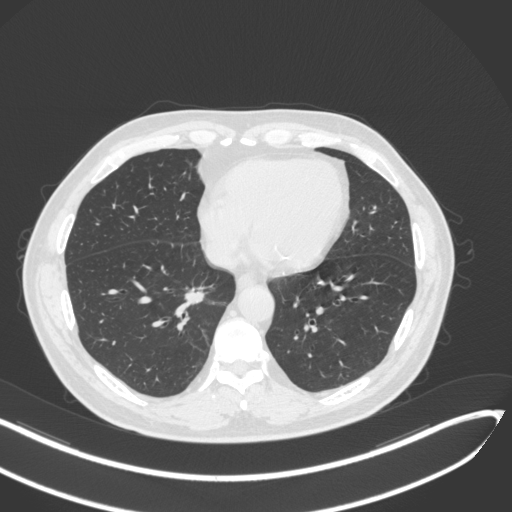
Chest CT, one axial slice; position 133 of 429 along the scan axis; reconstruction kernel B31f; lung window (W 1500 / L -600 HU); 1 mm slice thickness; 512 × 512 image matrix, field of view 400 × 400 mm. Male patient, age 62 years. Case-level facts recorded for this patient, not image findings: clinical TNM (as recorded): T1b N0 M0.
Annotated regions visible in this slice (bounding box drawn by a radiologist):
- lung tumour (recorded histology: adenocarcinoma): bounding box (x1, y1, x2, y2) in pixels: (183, 282, 209, 308)